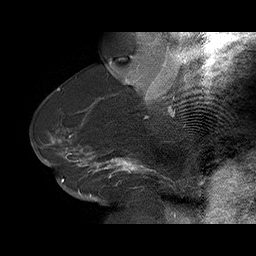
Breast MRI (dynamic contrast-enhanced), one sagittal slice. Slice 43 of 75 in the series (ordered by position). Dynamic contrast-enhanced series, time point 2 of 6 at this slice position (early post-contrast). 1.5 T. TE 4.5 ms, TR 32.4 ms. 3 mm slice thickness. 256 × 256 image matrix, field of view 180 × 180 mm. Female patient. From the clinical record (not read from this slice): setting: breast cancer imaged before/during neoadjuvant chemotherapy; receptor status: HR-positive, HER2-negative.
Annotated regions visible in this slice (semi-automatic segmentation, software-assisted and operator-edited):
- analysis volume of interest (the breast-tissue region the enhancement analysis was run in; not a lesion): bounding box <58,134,166,191> (left, top, right, bottom; pixels)
- tumour enhancement mask (voxels above the 100 % enhancement threshold inside the analysis volume of interest): <59,135,154,182>